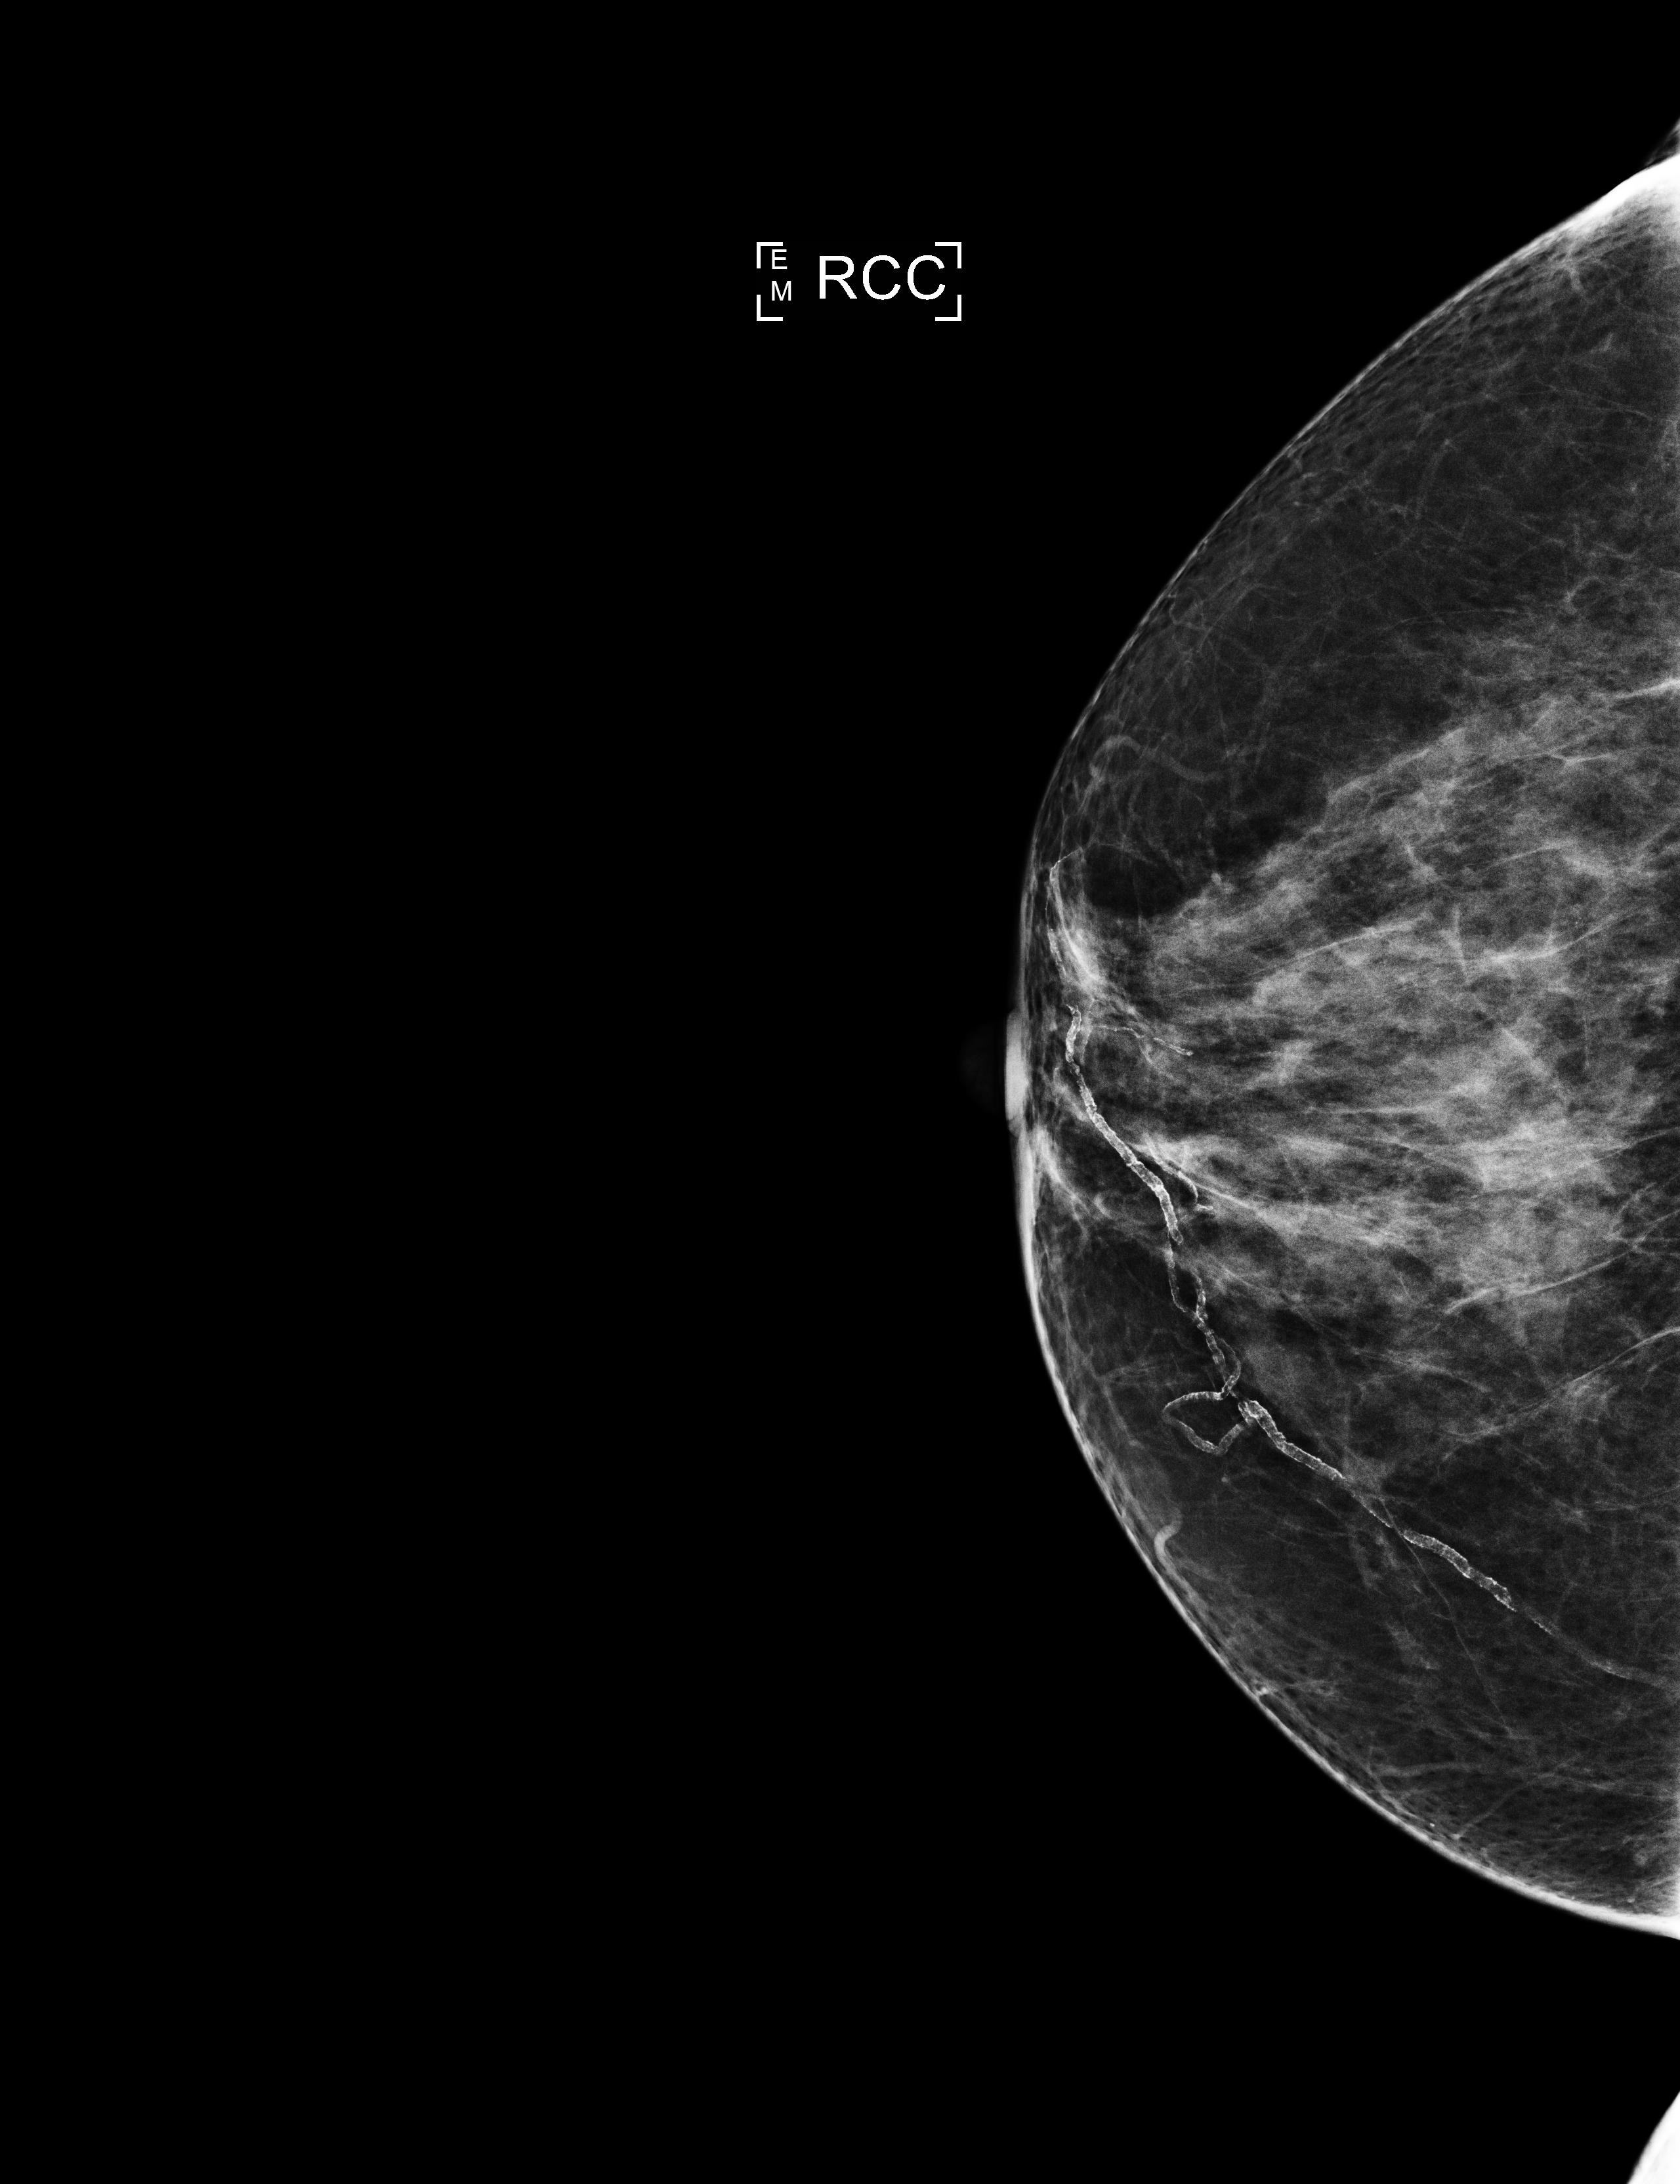
Full-field digital mammogram (FFDM); right breast; CC view; annual screening mammography examination; compressed breast thickness 54 mm. Patient: female, 59 years.
Breast density at the screening exam (both breasts): heterogeneously dense (BI-RADS density category c). Final BI-RADS category for the screening round (tomosynthesis exam, both breasts): category 1. Recall: no recall after this screen.